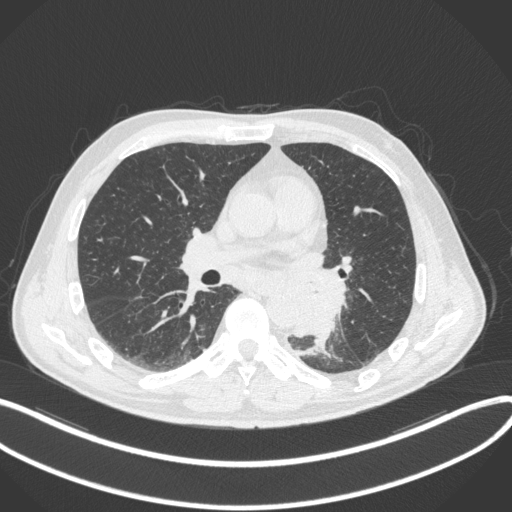
Chest CT, one axial slice. Slice 176 of 328 in the series (ordered by position). 120 kVp. Lung window (W 1500 / L -600 HU). 512 × 512 image matrix. Male patient, age 59 years. Case-level facts recorded for this patient, not image findings: clinical TNM (as recorded): T2a N2 M0.
Annotated regions visible in this slice (bounding box drawn by a radiologist):
- lung tumour (recorded histology: squamous cell carcinoma): box from (x=293, y=263) to (x=353, y=342) px